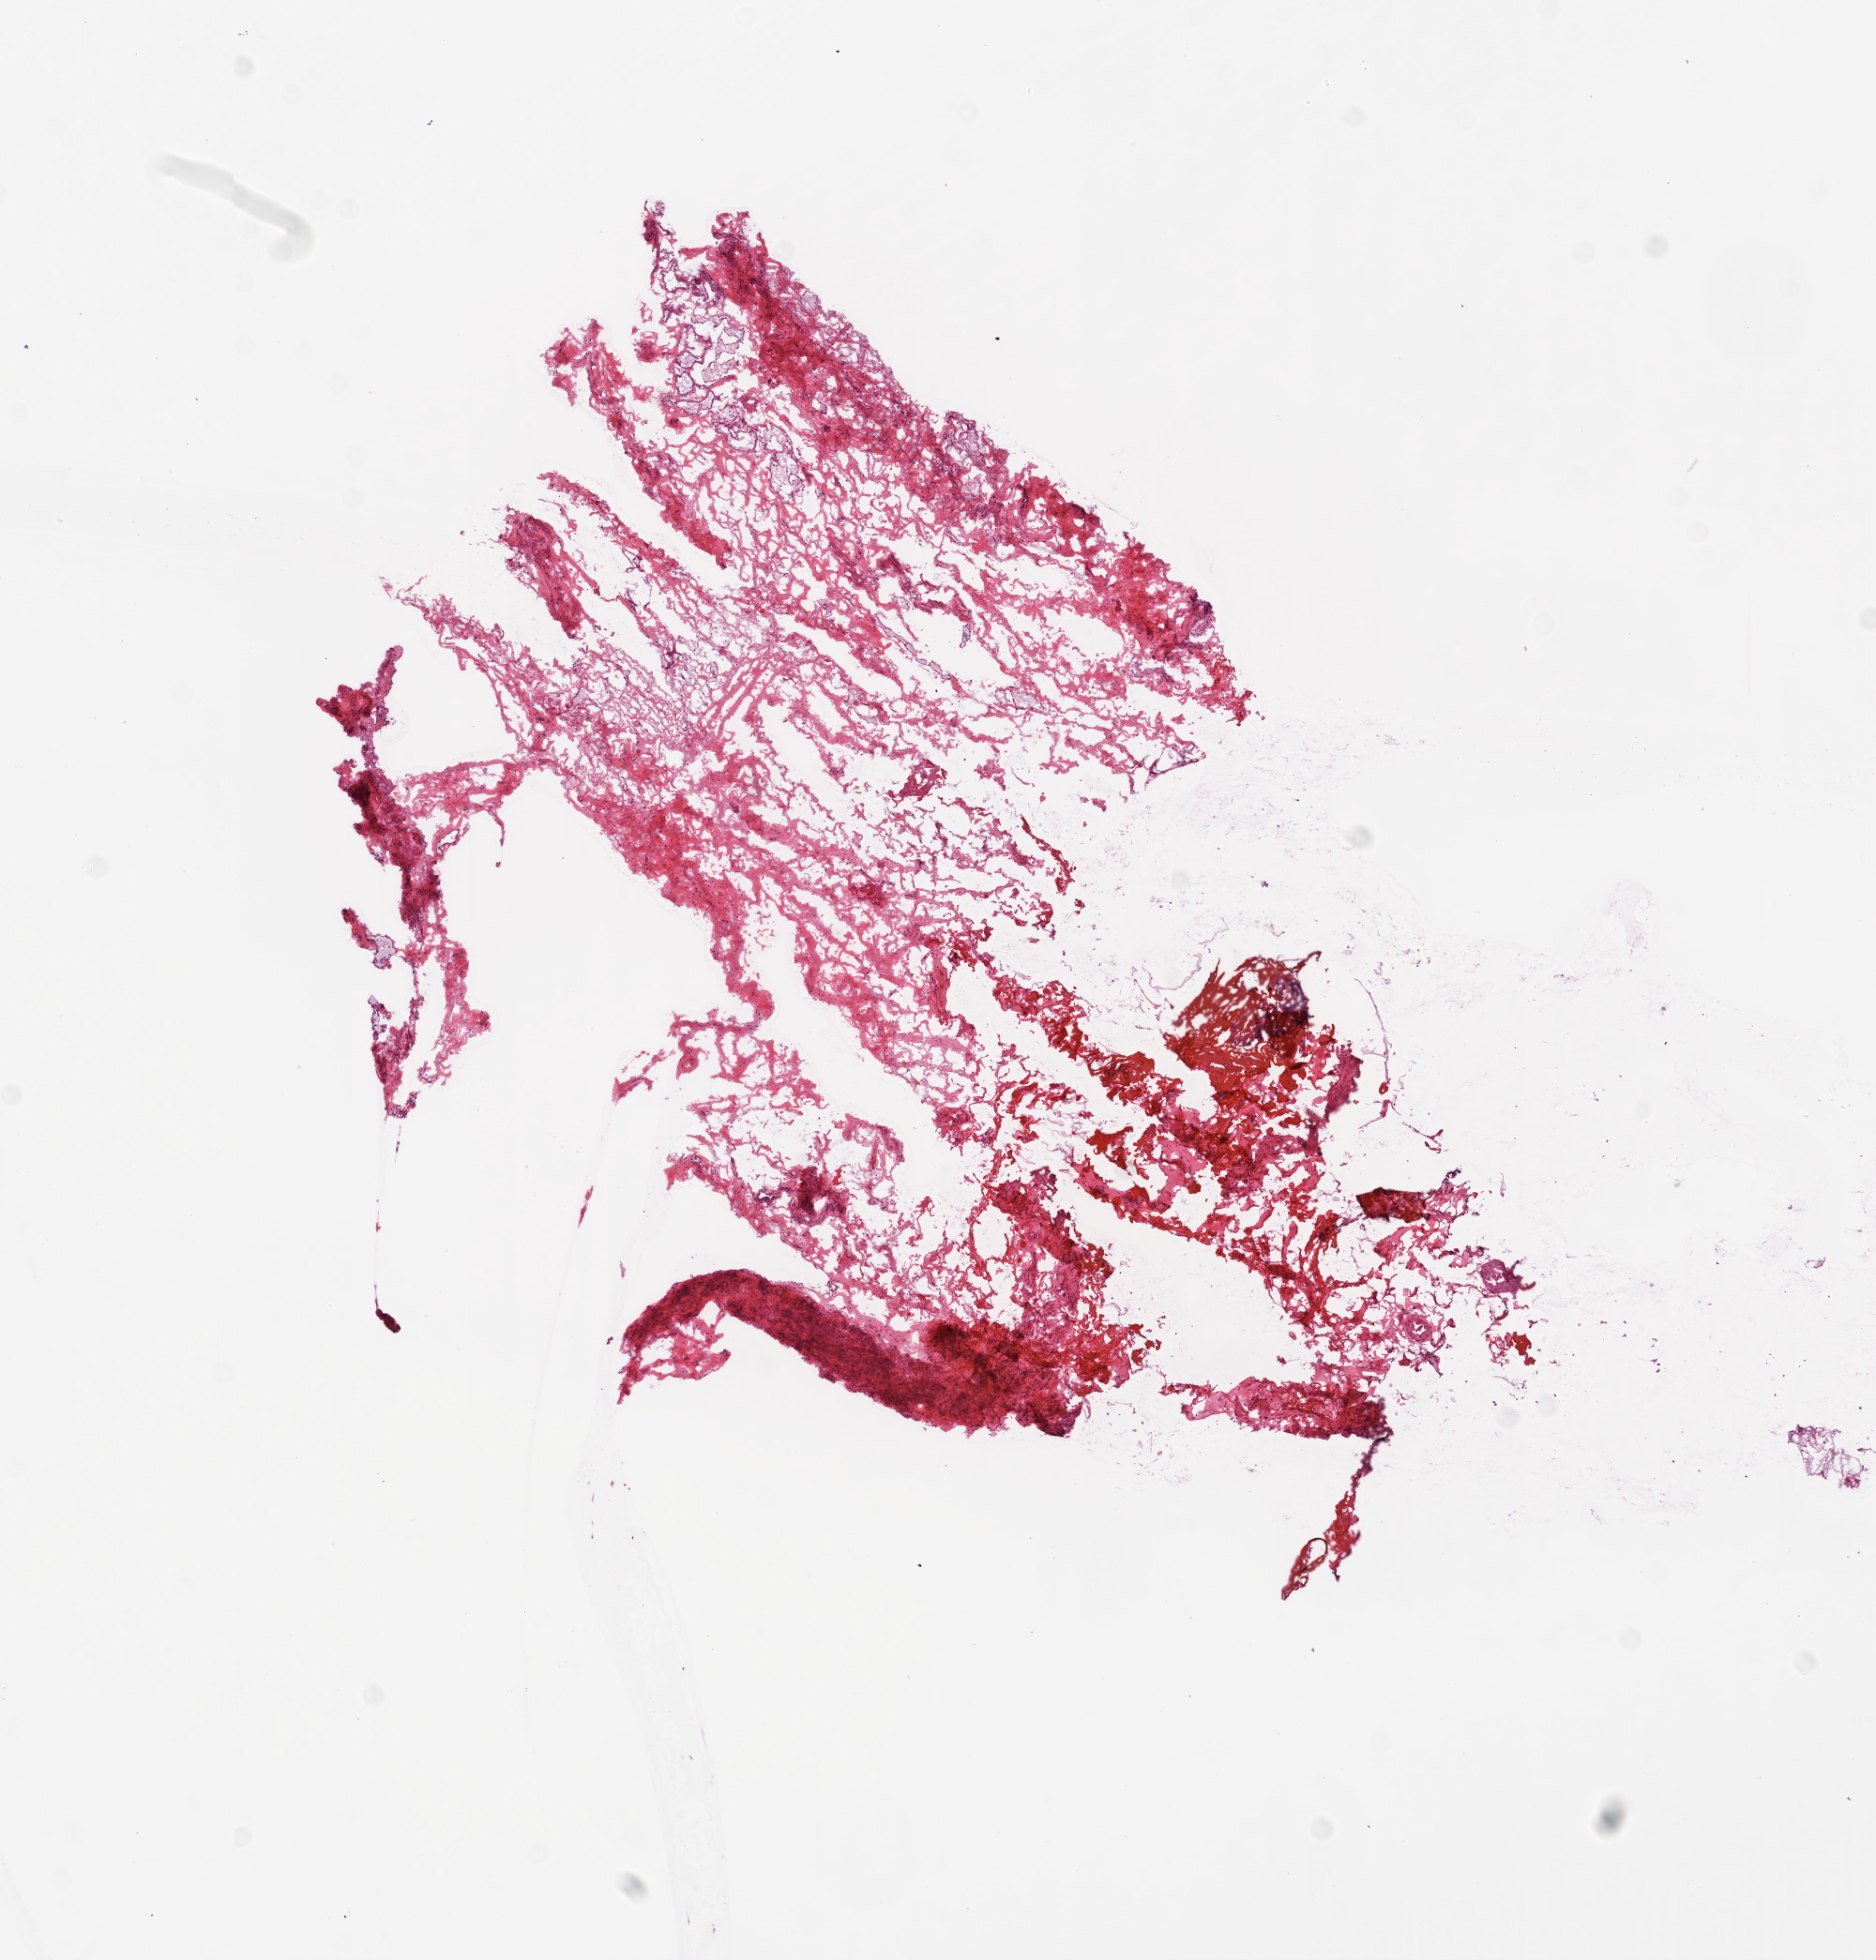
Digitized H&E-stained tissue section (whole slide), whole scanned area (about 8.0 x 8.4 mm) shown as a low-resolution overview, frozen section from the bottom of the tissue portion, sample: solid tissue normal (non-tumour tissue), ovary. Female, age 54 years at initial diagnosis.
This section: solid tissue normal sample (biorepository sample class). Patient diagnosis: Serous cystadenocarcinoma, NOS.